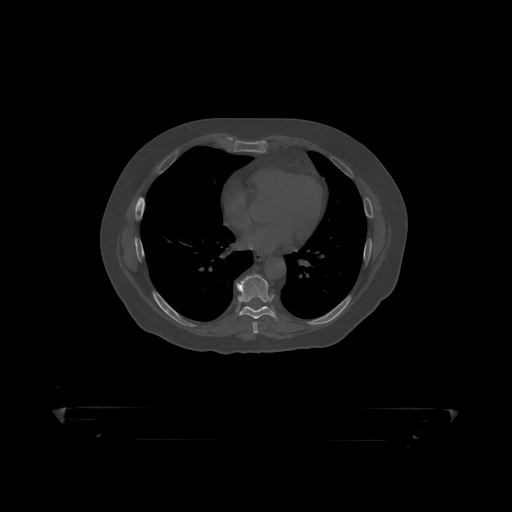
CT including the spine, one axial slice; slice 258 of 390 in the series (ordered by position); reconstruction kernel STANDARD; bone window (W 1800 / L 400 HU); 1.25 mm slice thickness; 512 × 512 image matrix, field of view 650 × 650 mm. Patient: male, 60 years. From the clinical record (not read from this slice): primary cancer: prostate.
Structures marked on this image (semi-automatically segmented with operator editing):
- T8 vertebra: bounding box [x1, y1, x2, y2] px = [235, 275, 276, 319]
- T9 vertebra: [246, 306, 250, 308]